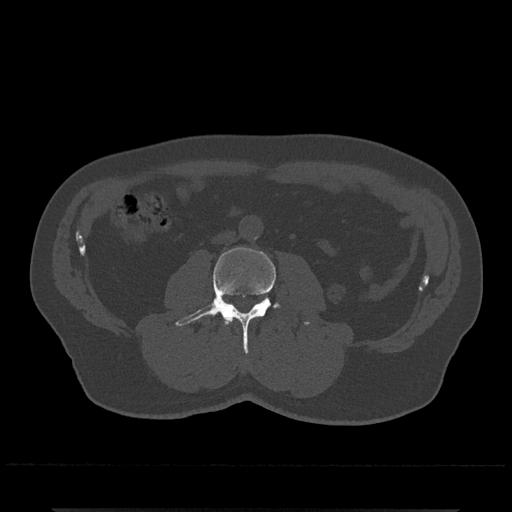
CT including the spine, one axial slice. Position 221 of 797 along the scan axis. 120 kVp. Bone window (W 1800 / L 400 HU). 0.5 mm slice thickness. 512 × 512 image matrix, field of view 393 × 393 mm. Patient: male, 67 years. Case-level facts recorded for this patient, not image findings: primary cancer: prostate.
Structures marked on this image (semi-automatic segmentation, software-assisted and operator-edited):
- L2 vertebra: bounding box (x1, y1, x2, y2) in pixels: (225, 319, 232, 324)
- L3 vertebra: (175, 247, 311, 354)